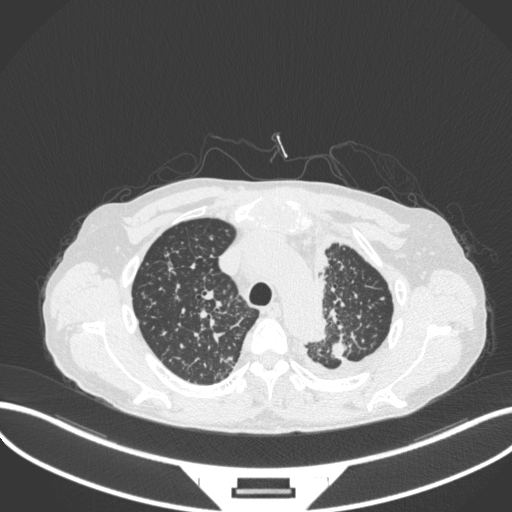
Chest CT, one axial slice; position 274 of 319 along the scan axis; 120 kVp; lung window (W 1500 / L -600 HU); 1 mm slice thickness; 512 × 512 image matrix. Patient: male, 58 years. Case-level facts recorded for this patient, not image findings: clinical TNM (as recorded): T1c N3 M1.
Structures marked on this image (rectangle marked by the reading radiologist):
- lung tumour (recorded histology: adenocarcinoma): bounding box [x1, y1, x2, y2] px = [324, 335, 349, 363]